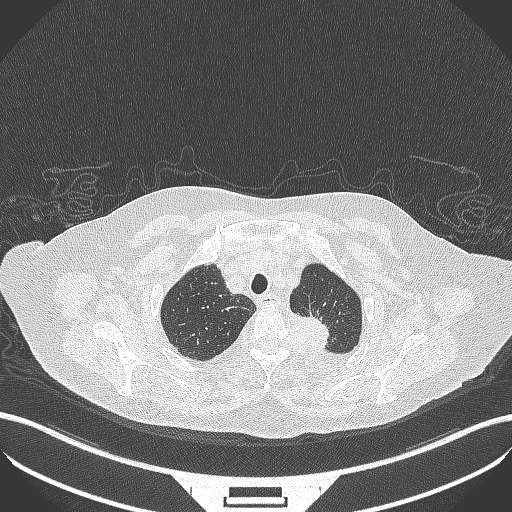
Chest CT, one axial slice. Position 298 of 353 along the scan axis. Reconstruction kernel B70f. Lung window (W 1500 / L -600 HU). 1 mm slice thickness. 512 × 512 image matrix, field of view 400 × 400 mm. Female patient, age 81 years. From the clinical record (not read from this slice): clinical TNM (as recorded): T2a N0 M0.
Structures marked on this image (rectangle marked by the reading radiologist):
- lung tumour (recorded histology: adenocarcinoma): box from (x=280, y=305) to (x=333, y=352) px